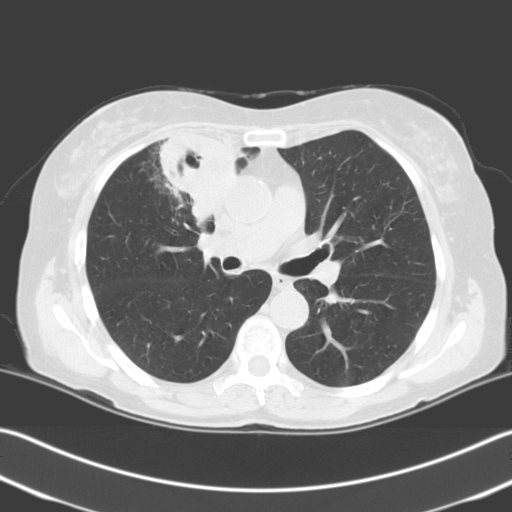
Low-dose screening chest CT, one axial slice; slice 129 of 204 in the series (ordered by position); 140 kVp; lung window (W 1500 / L -600 HU); 3.2 mm slice thickness; 512 × 512 image matrix.
Structures marked on this image (manually delineated by an expert):
- lesion 1 (tumor, upper lobe of right lung): bounding box (x1, y1, x2, y2) in pixels: (159, 133, 246, 225)